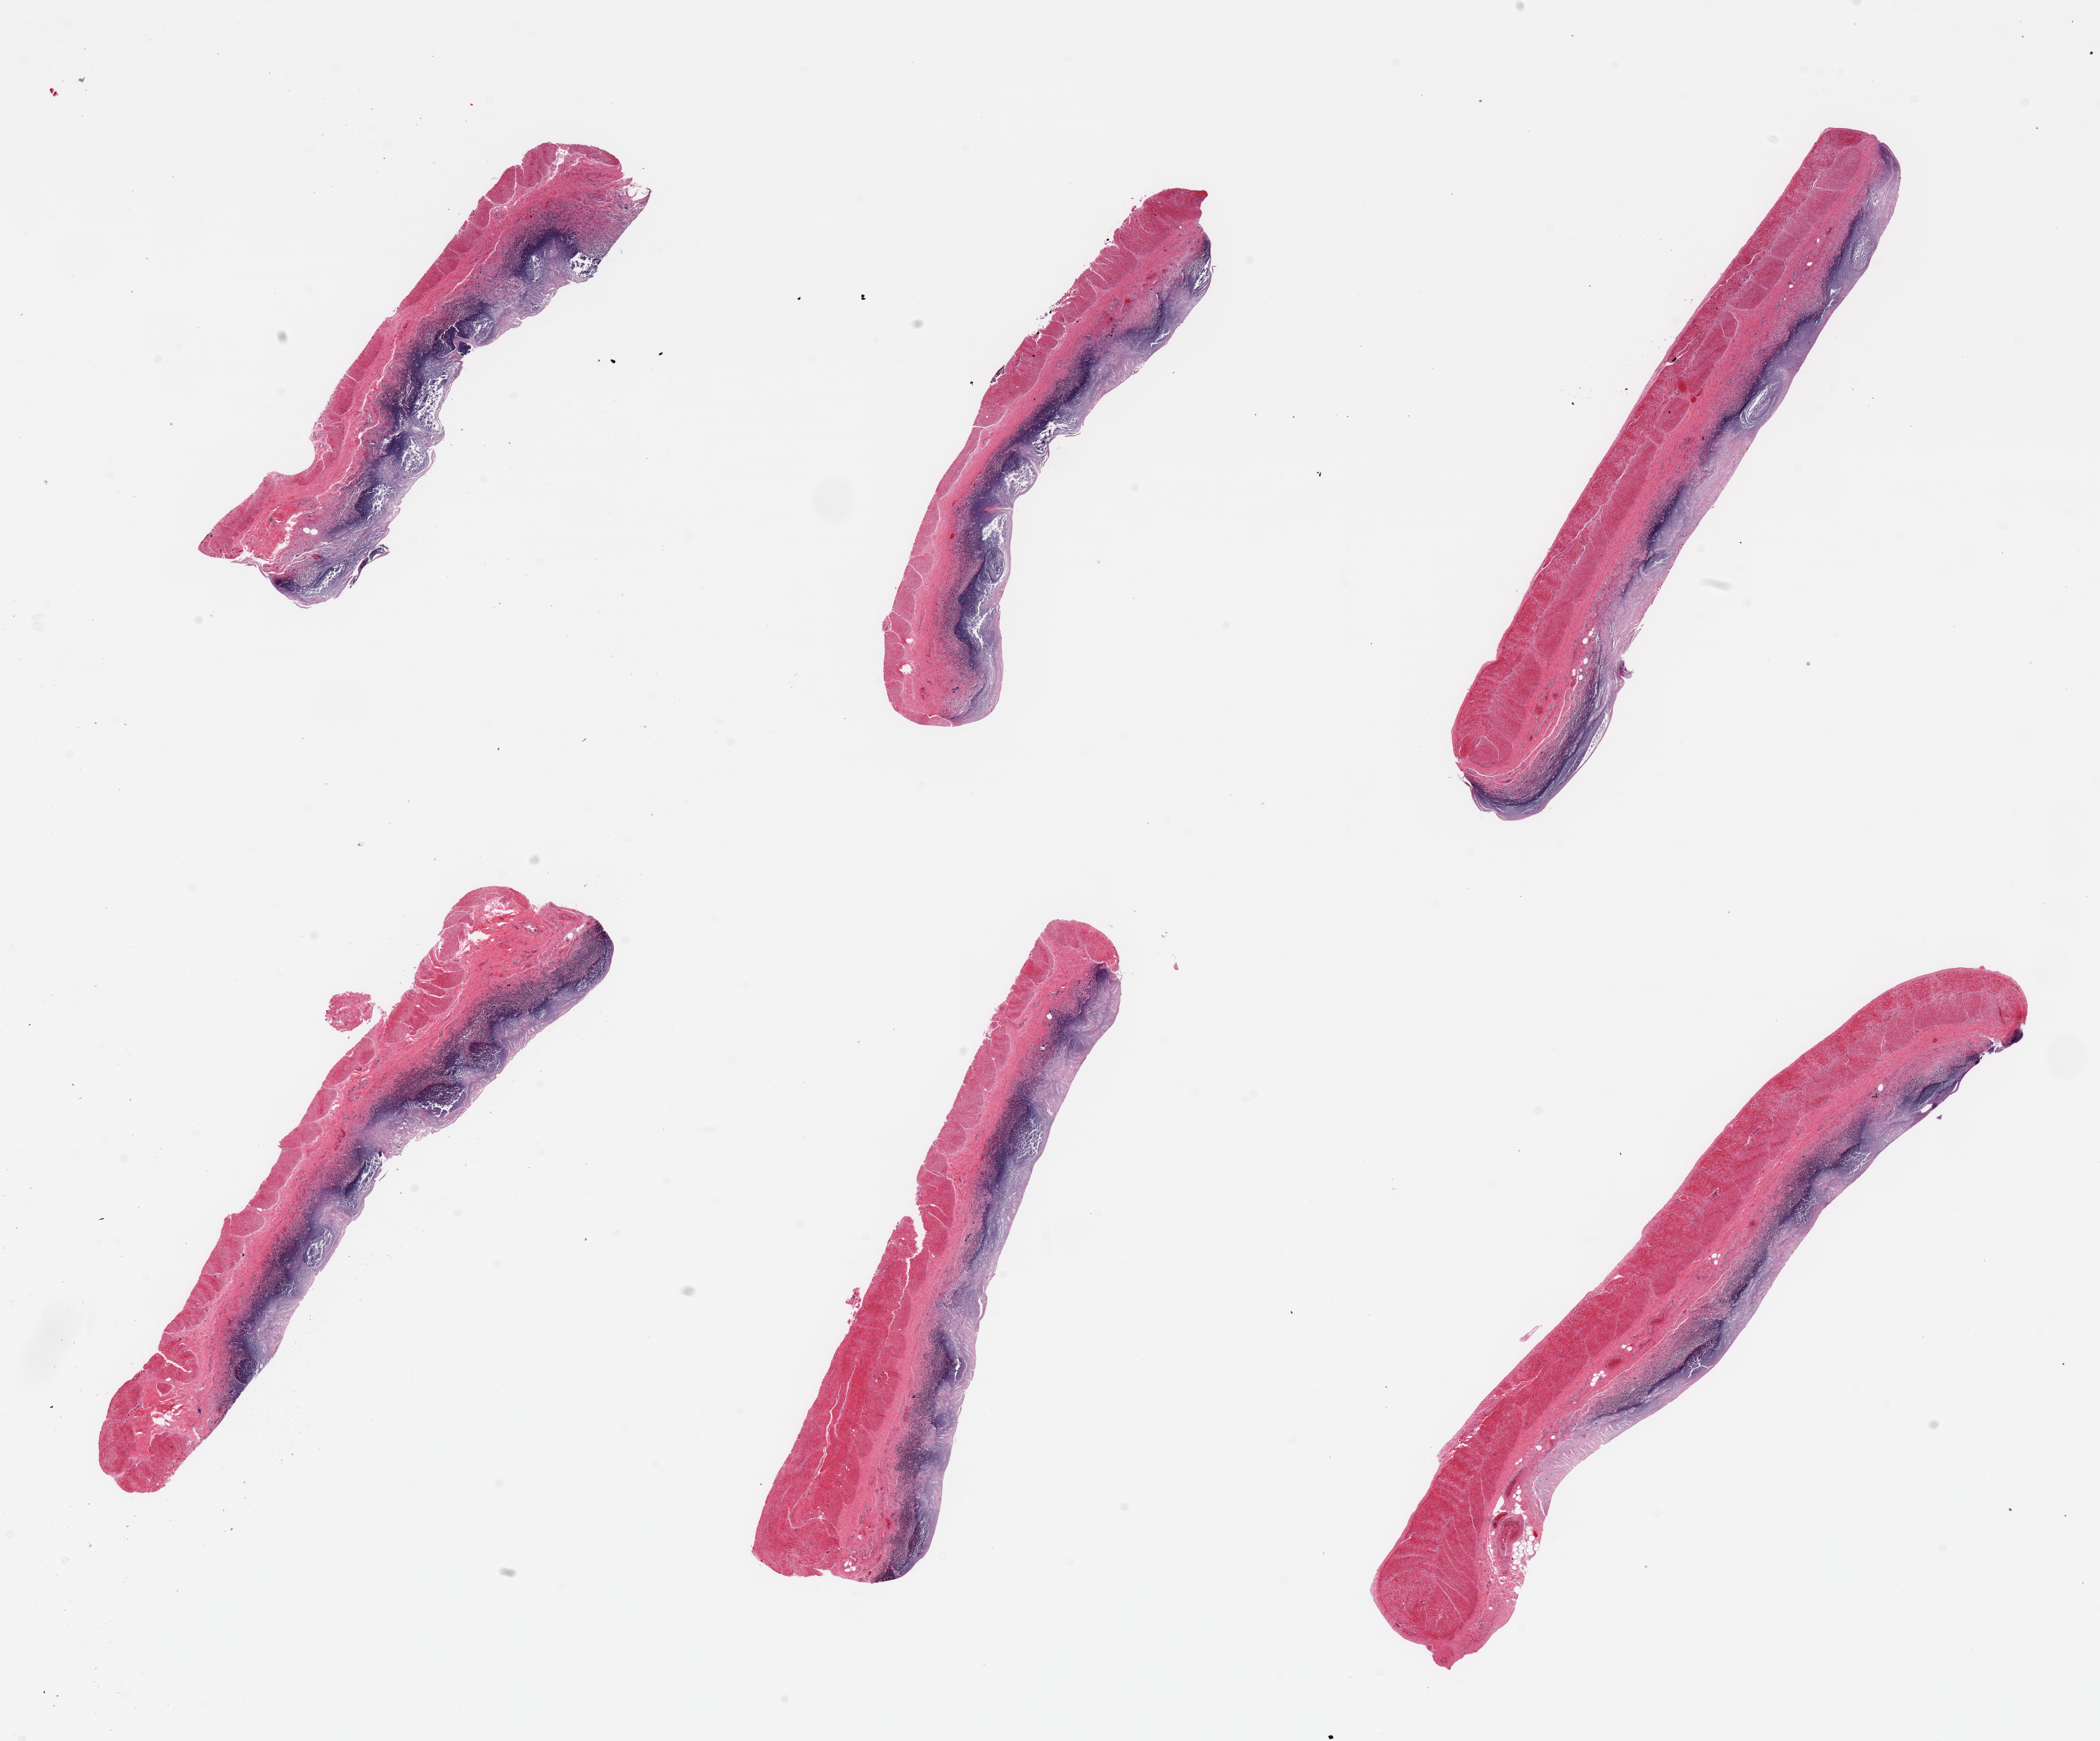
Whole-slide image, haematoxylin and eosin stain, brightfield — shown as a low-resolution overview of the whole scanned area (about 23.6 x 19.6 mm), PAXgene-fixed, paraffin-embedded tissue, target tissue: ileum, donor tissue sample. Donor sex: male.
Reviewer comment on this tissue sample: 6 pieces, glandular elments autolyzed; residucal viable lymphoid aggregates are ~30% tissue.